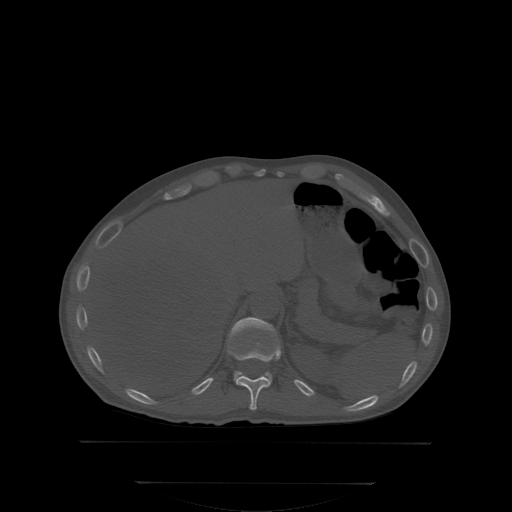
CT including the spine, one axial slice; slice 177 of 350 in the series (ordered by position); bone window (W 1800 / L 400 HU); 2.5 mm slice thickness; 512 × 512 image matrix. Patient: male, 58 years. From the clinical record (not read from this slice): primary cancer: prostate; vertebrae with lytic lesions (as recorded): L1.
Annotated regions visible in this slice (semi-automatic segmentation, software-assisted and operator-edited):
- T11 vertebra: bounding box [x1, y1, x2, y2] px = [229, 344, 280, 410]
- T12 vertebra: [229, 318, 276, 376]